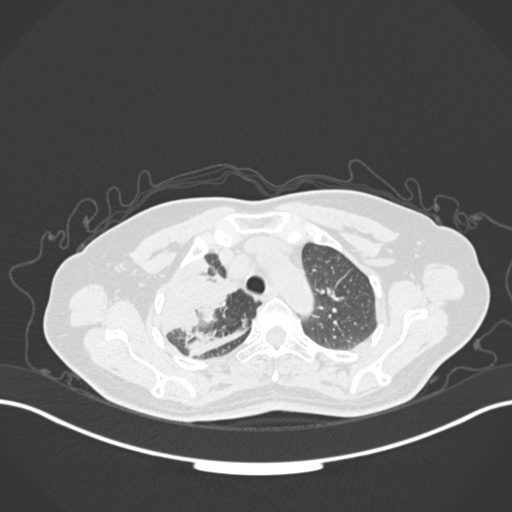
Chest CT, one axial slice; slice 127 of 177 in the series (ordered by position); reconstruction kernel B30f; 120 kVp; lung window (W 1500 / L -600 HU); 1 mm slice thickness; 512 × 512 image matrix, field of view 400 × 400 mm. Patient: female, 60 years. Case-level facts recorded for this patient, not image findings: clinical TNM (as recorded): T3 N1 M1.
Outlined on this slice (bounding box drawn by a radiologist):
- lung tumour (recorded histology: adenocarcinoma): bounding box [x1, y1, x2, y2] px = [144, 252, 244, 339]